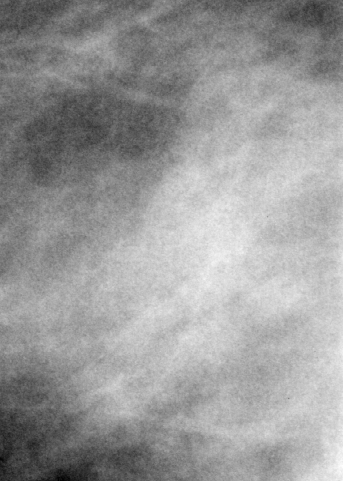
Cropped region of a digitized screen-film mammogram centred on a radiologist-marked abnormality; right breast; MLO view; BI-RADS breast density category 2 (scale 1–4).
Finding: mass, shape irregular, margins ill defined; BI-RADS assessment category 4; subtlety rating 5 on a 1 (subtle) to 5 (obvious) scale; pathology (as recorded): benign.